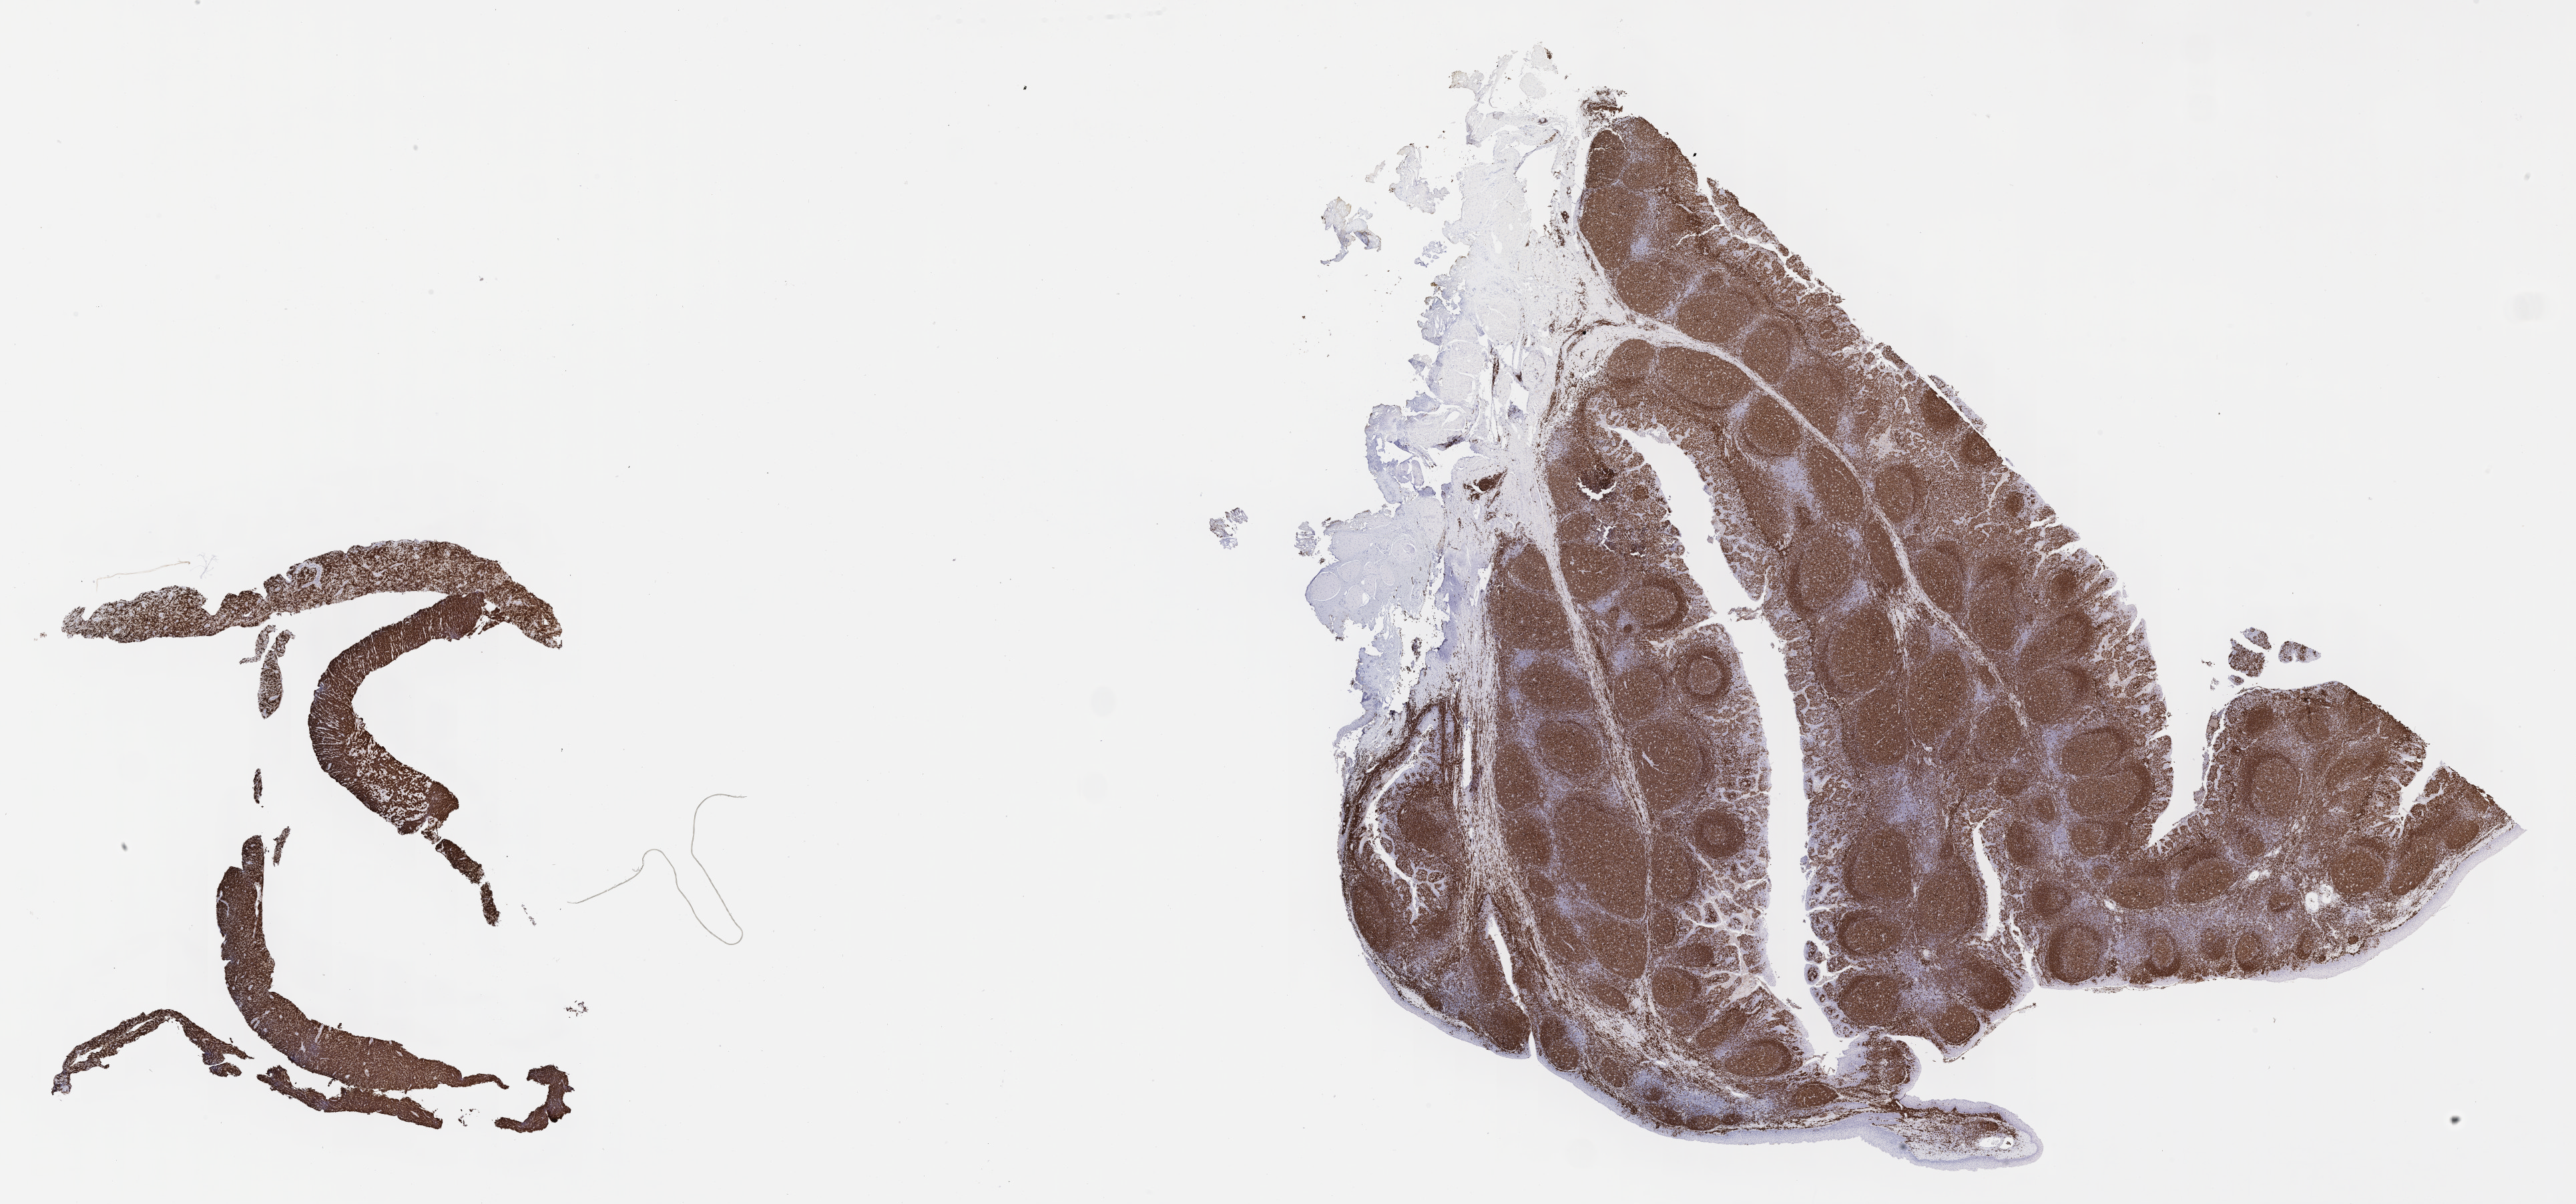
IHC for CD79a, whole-slide image — a low-resolution overview of the entire scanned area, about 31.2 x 14.6 mm. Tumor tissue. Site: pleura. Male patient; age at initial diagnosis 2 years.
Histologic diagnosis: Diffuse large B-cell lymphoma, NOS.